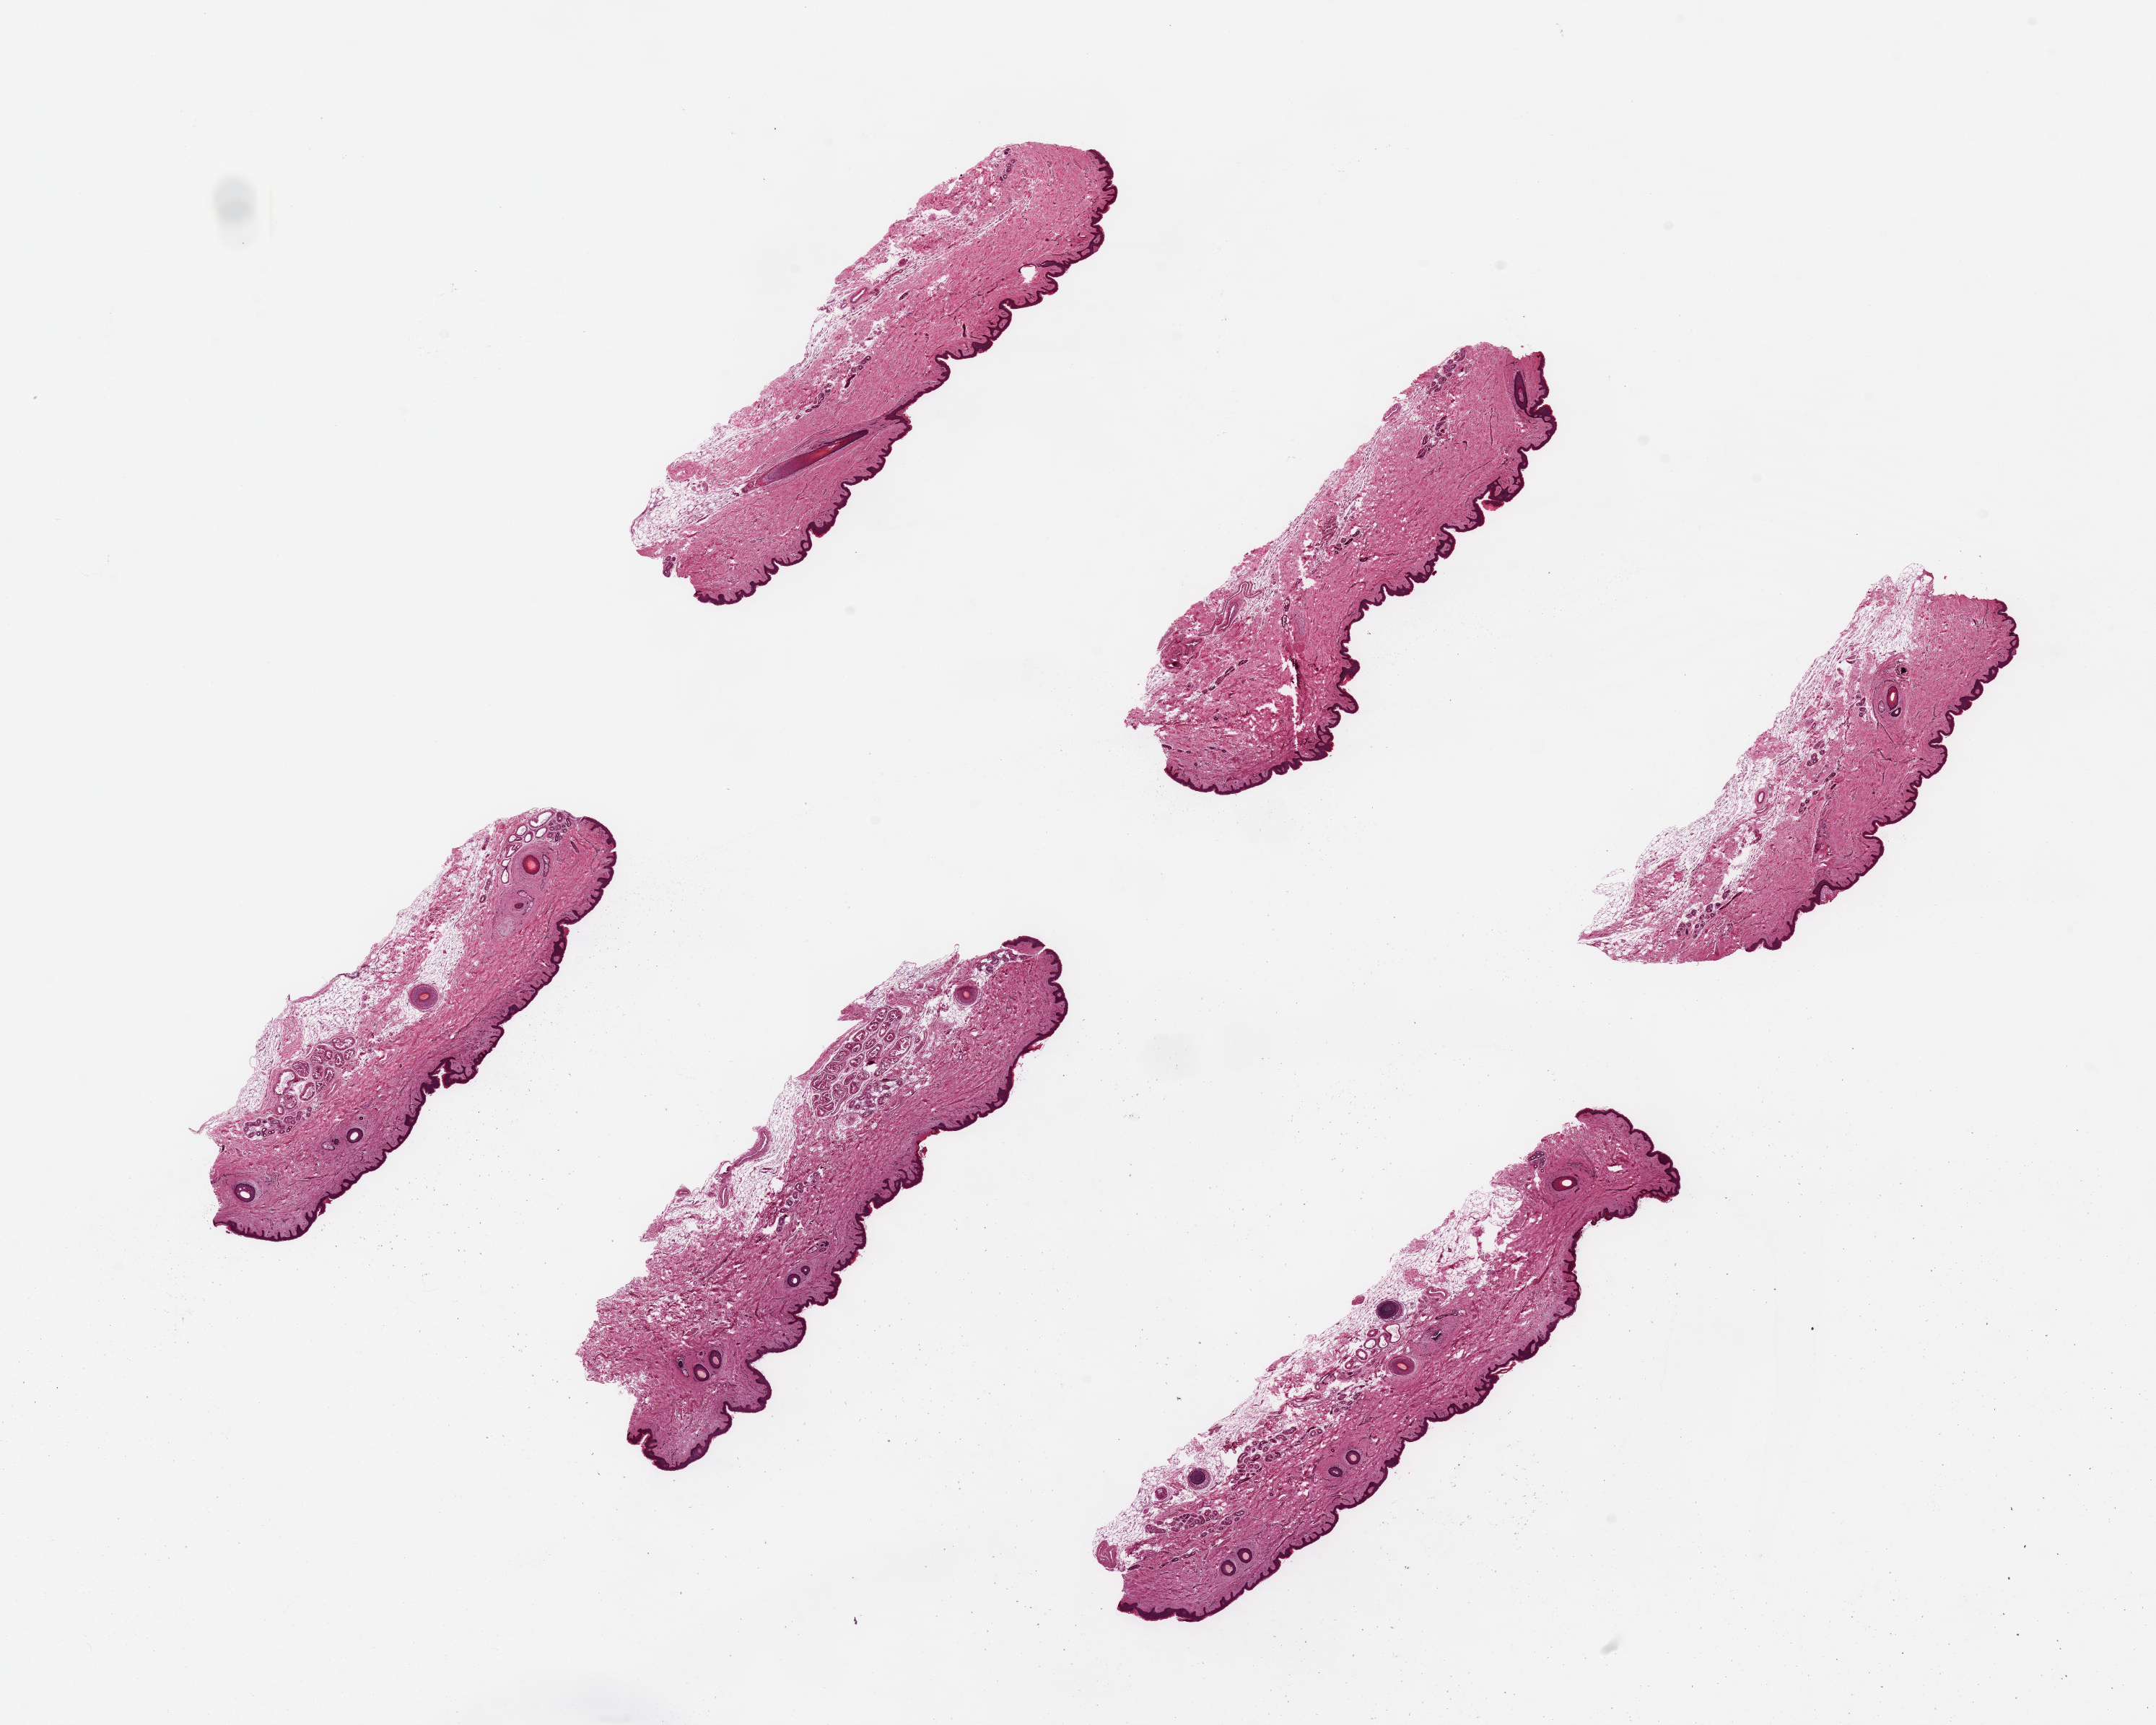
H&E whole-slide image, whole scanned area (about 23.6 x 18.9 mm) shown as a low-resolution overview, PAXgene-fixed paraffin-embedded (PFPE) section, section of skin of suprapubic region (target tissue), donor tissue sample.
Pathologist's review note for this sample: 6 pieces, up to 8x2mm.